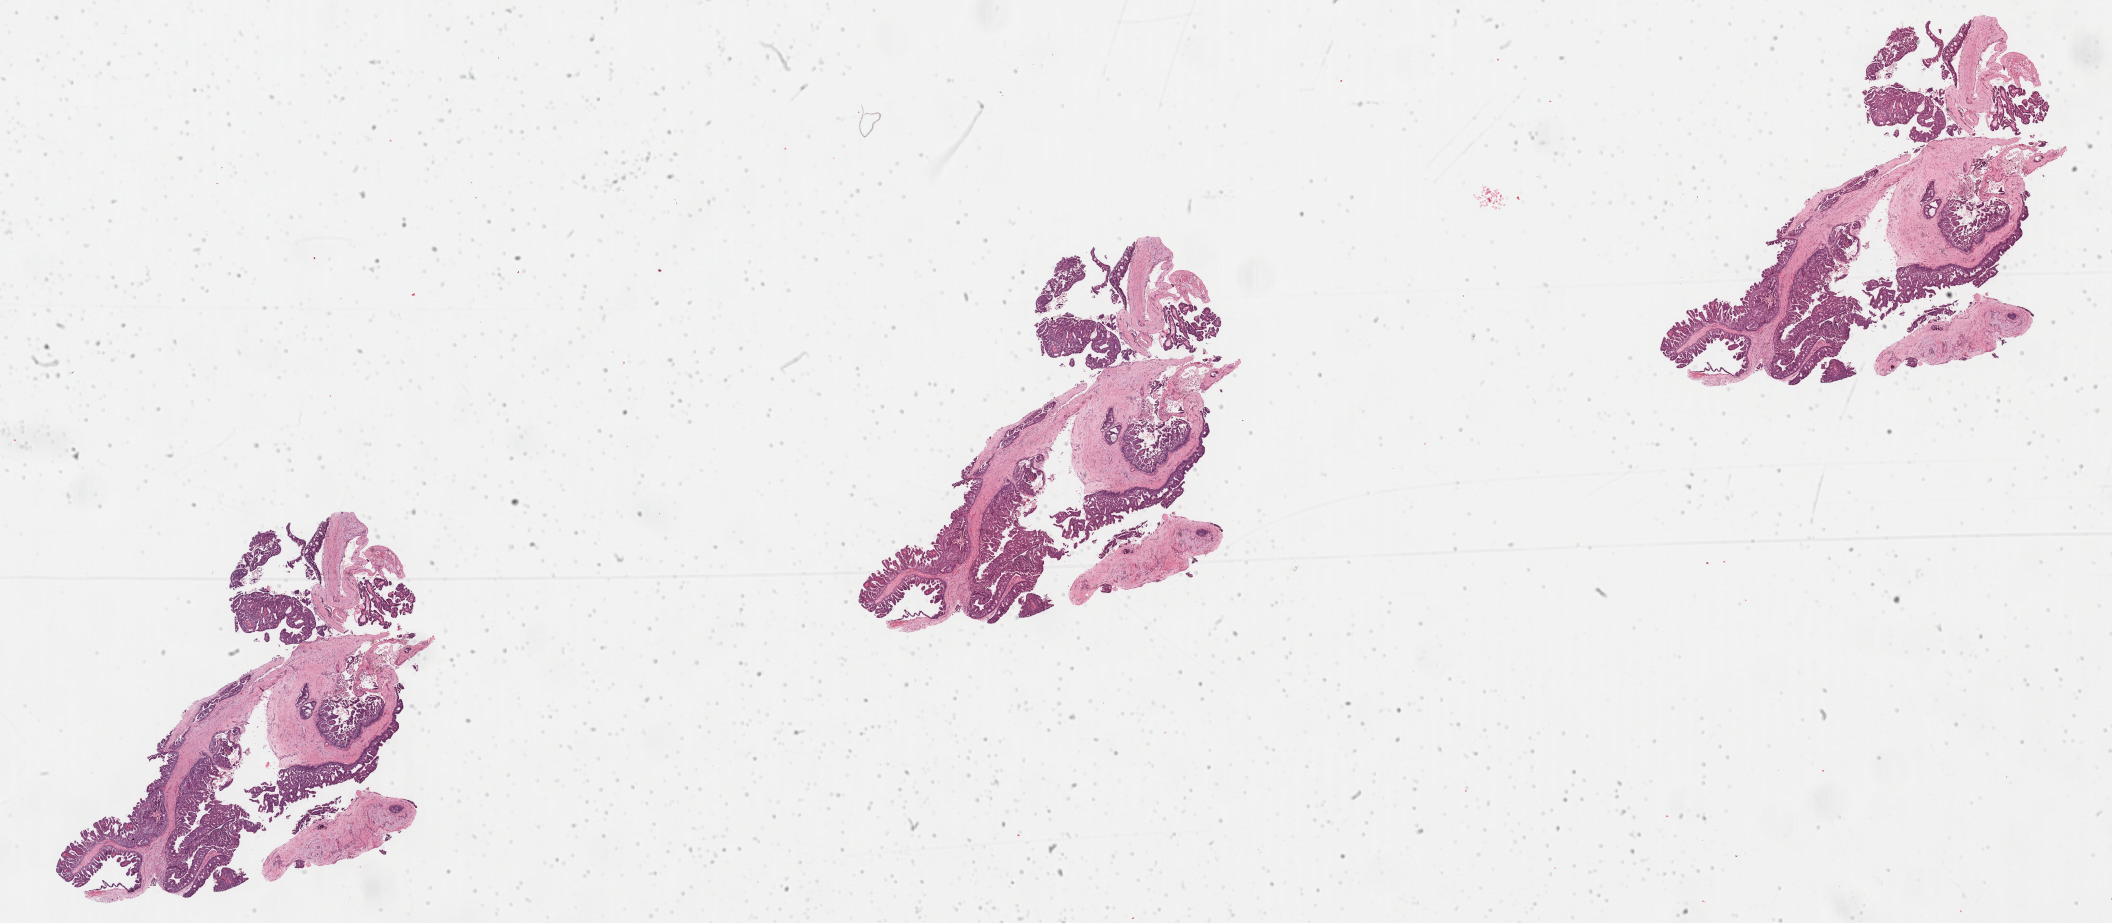
Digitized Hematoxylin and eosin (H&E) stained tissue section (whole slide), whole scanned area (about 33.4 x 14.6 mm) shown as a low-resolution overview, formalin-fixed paraffin-embedded (FFPE) diagnostic section, sample: primary tumour, breast. Patient: female, age at initial diagnosis 63 years.
AJCC pathologic stage: IA. Diagnosis: Infiltrating duct carcinoma, NOS.